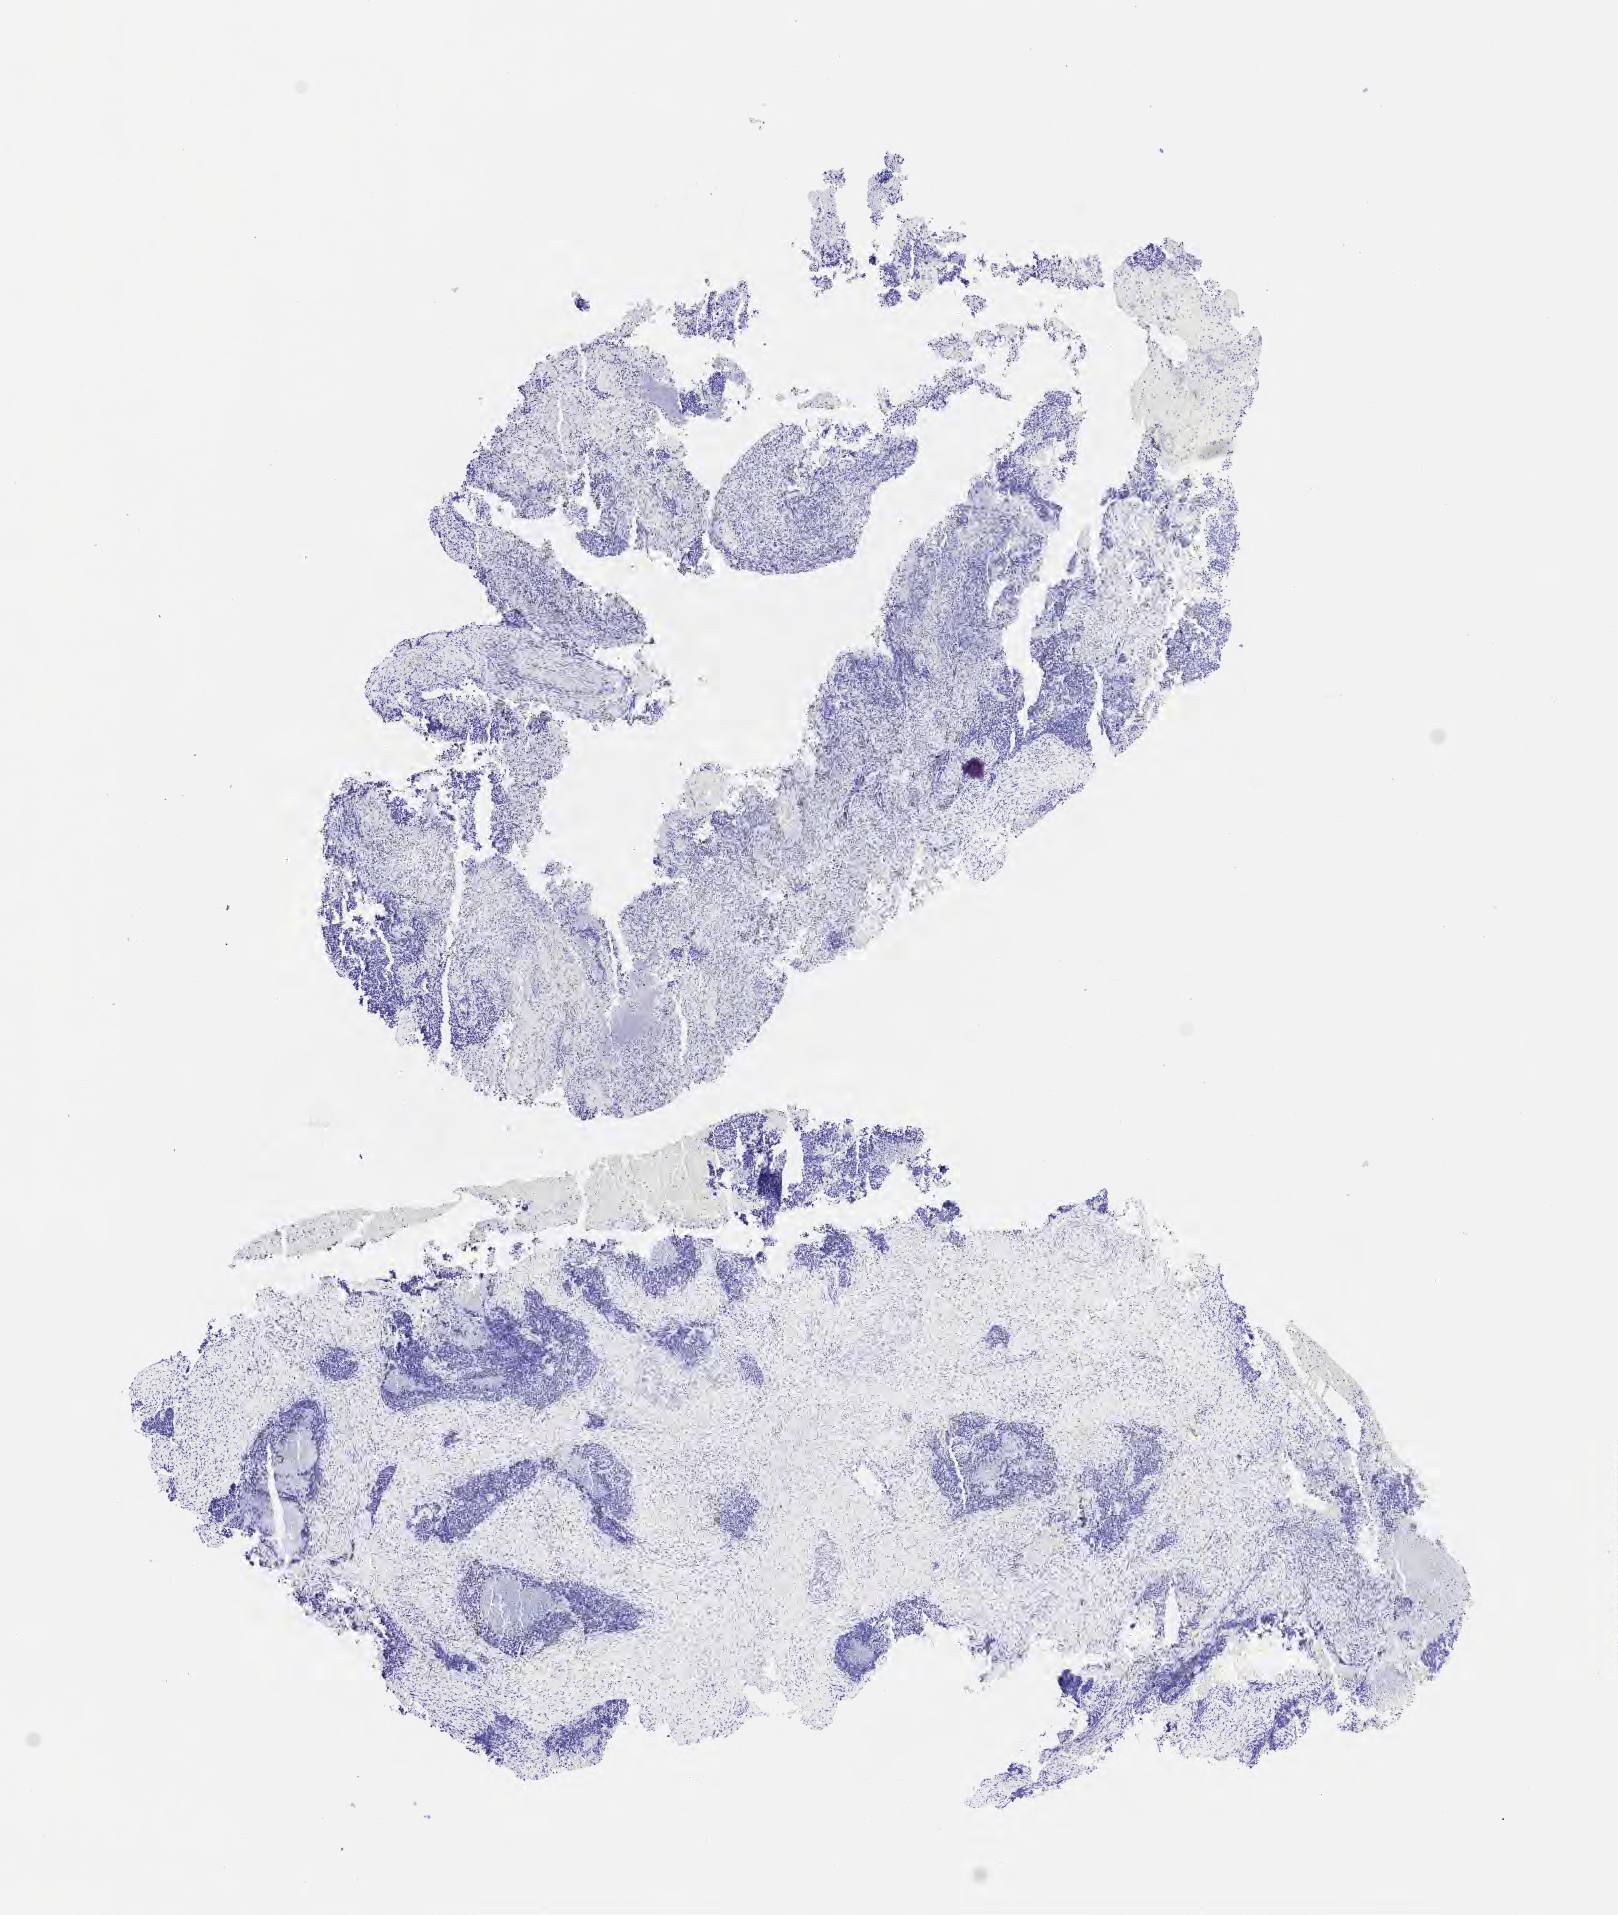
Immunohistochemistry (IHC) whole-slide image stained for chromogranin, shown as a low-resolution overview of the whole scanned area (about 6.5 x 7.7 mm), tumor tissue, site: cervix. Female patient, aged 47.
Histologic diagnosis: Squamous cell carcinoma, large cell, nonkeratinizing, NOS.